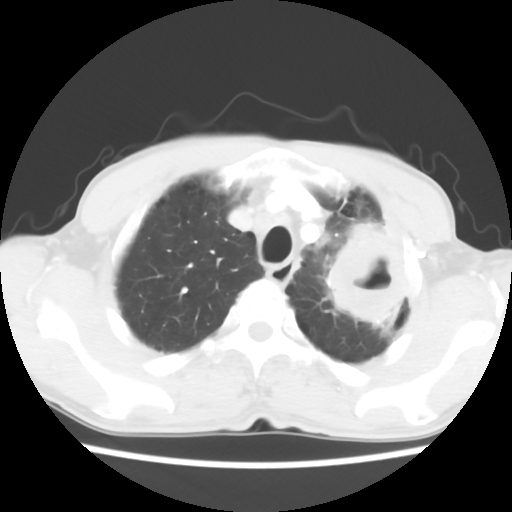
Chest CT, one axial slice. 120 kVp. Lung window (W 1500 / L -600 HU). 5 mm slice thickness. 512 × 512 image matrix, field of view 308 × 308 mm. Patient: male, 64 years. Case-level facts recorded for this patient, not image findings: clinical TNM (as recorded): T3 N3 M0; histopathological grade: G3.
Annotated regions visible in this slice (rectangle marked by the reading radiologist):
- lung tumour (recorded histology: adenocarcinoma): bounding box <314,213,414,339> (left, top, right, bottom; pixels)